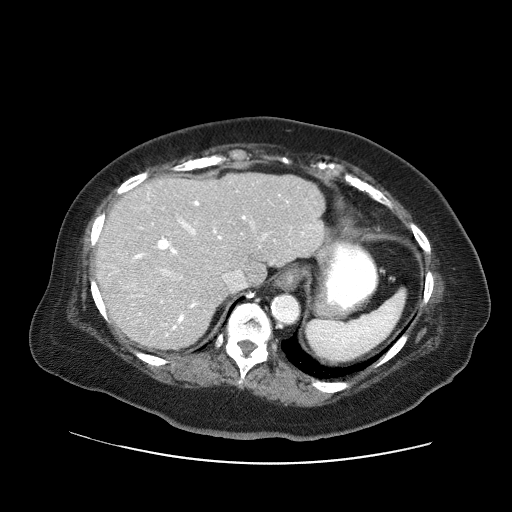
Contrast-enhanced abdominal CT (liver protocol), one axial slice; slice 44 of 71 in the series (ordered by position); soft-tissue window (W 400 / L 40 HU); 512 × 512 image matrix, field of view 400 × 400 mm. Case-level facts recorded for this patient, not image findings: diagnosis: hepatocellular carcinoma (patient treated with transarterial chemoembolisation; whether this scan precedes or follows treatment is not stated here); TNM stage (as recorded): Stage-II; Child-Pugh class: A; tumour differentiation: poorly differentiated.
Structures marked on this image (semi-automatically segmented with operator editing):
- liver parenchyma outside the tumour (the mass and vessels are separate outlines, so this box may not span the whole liver): box from (x=96, y=172) to (x=324, y=350) px
- liver vessels: (x=110, y=193)–(x=311, y=336)